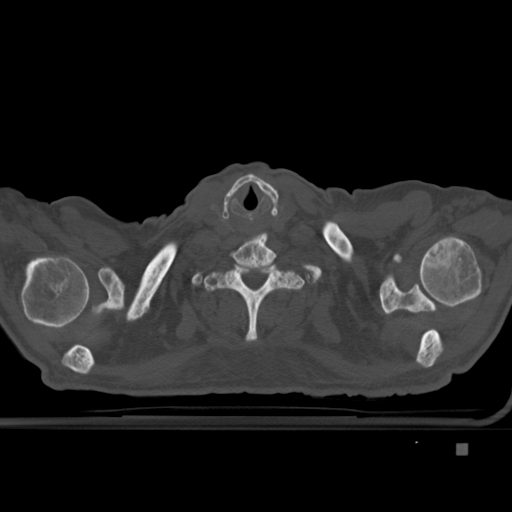
CT including the spine, one axial slice; slice 362 of 451 in the series (ordered by position); bone window (W 1800 / L 400 HU); 1.5 mm slice thickness; 512 × 512 image matrix, field of view 378 × 378 mm. Patient: male, 75 years. Case-level facts recorded for this patient, not image findings: primary cancer: prostate.
Outlined on this slice (semi-automatically segmented with operator editing):
- T1 vertebra: box from (x=204, y=261) to (x=305, y=342) px